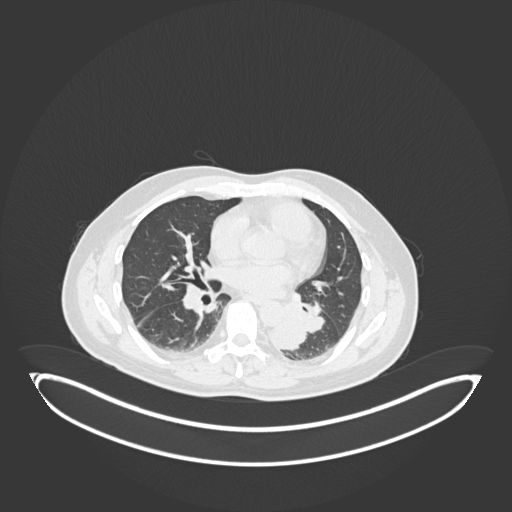
Chest CT, one axial slice; slice 91 of 258 in the series (ordered by position); reconstruction kernel B30f; 120 kVp; lung window (W 1500 / L -600 HU); 512 × 512 image matrix, field of view 500 × 500 mm. Male patient, age 54 years. Case-level facts recorded for this patient, not image findings: clinical TNM (as recorded): T3 N0 M0.
Outlined on this slice (rectangle marked by the reading radiologist):
- lung tumour (recorded histology: squamous cell carcinoma): box from (x=265, y=303) to (x=308, y=351) px